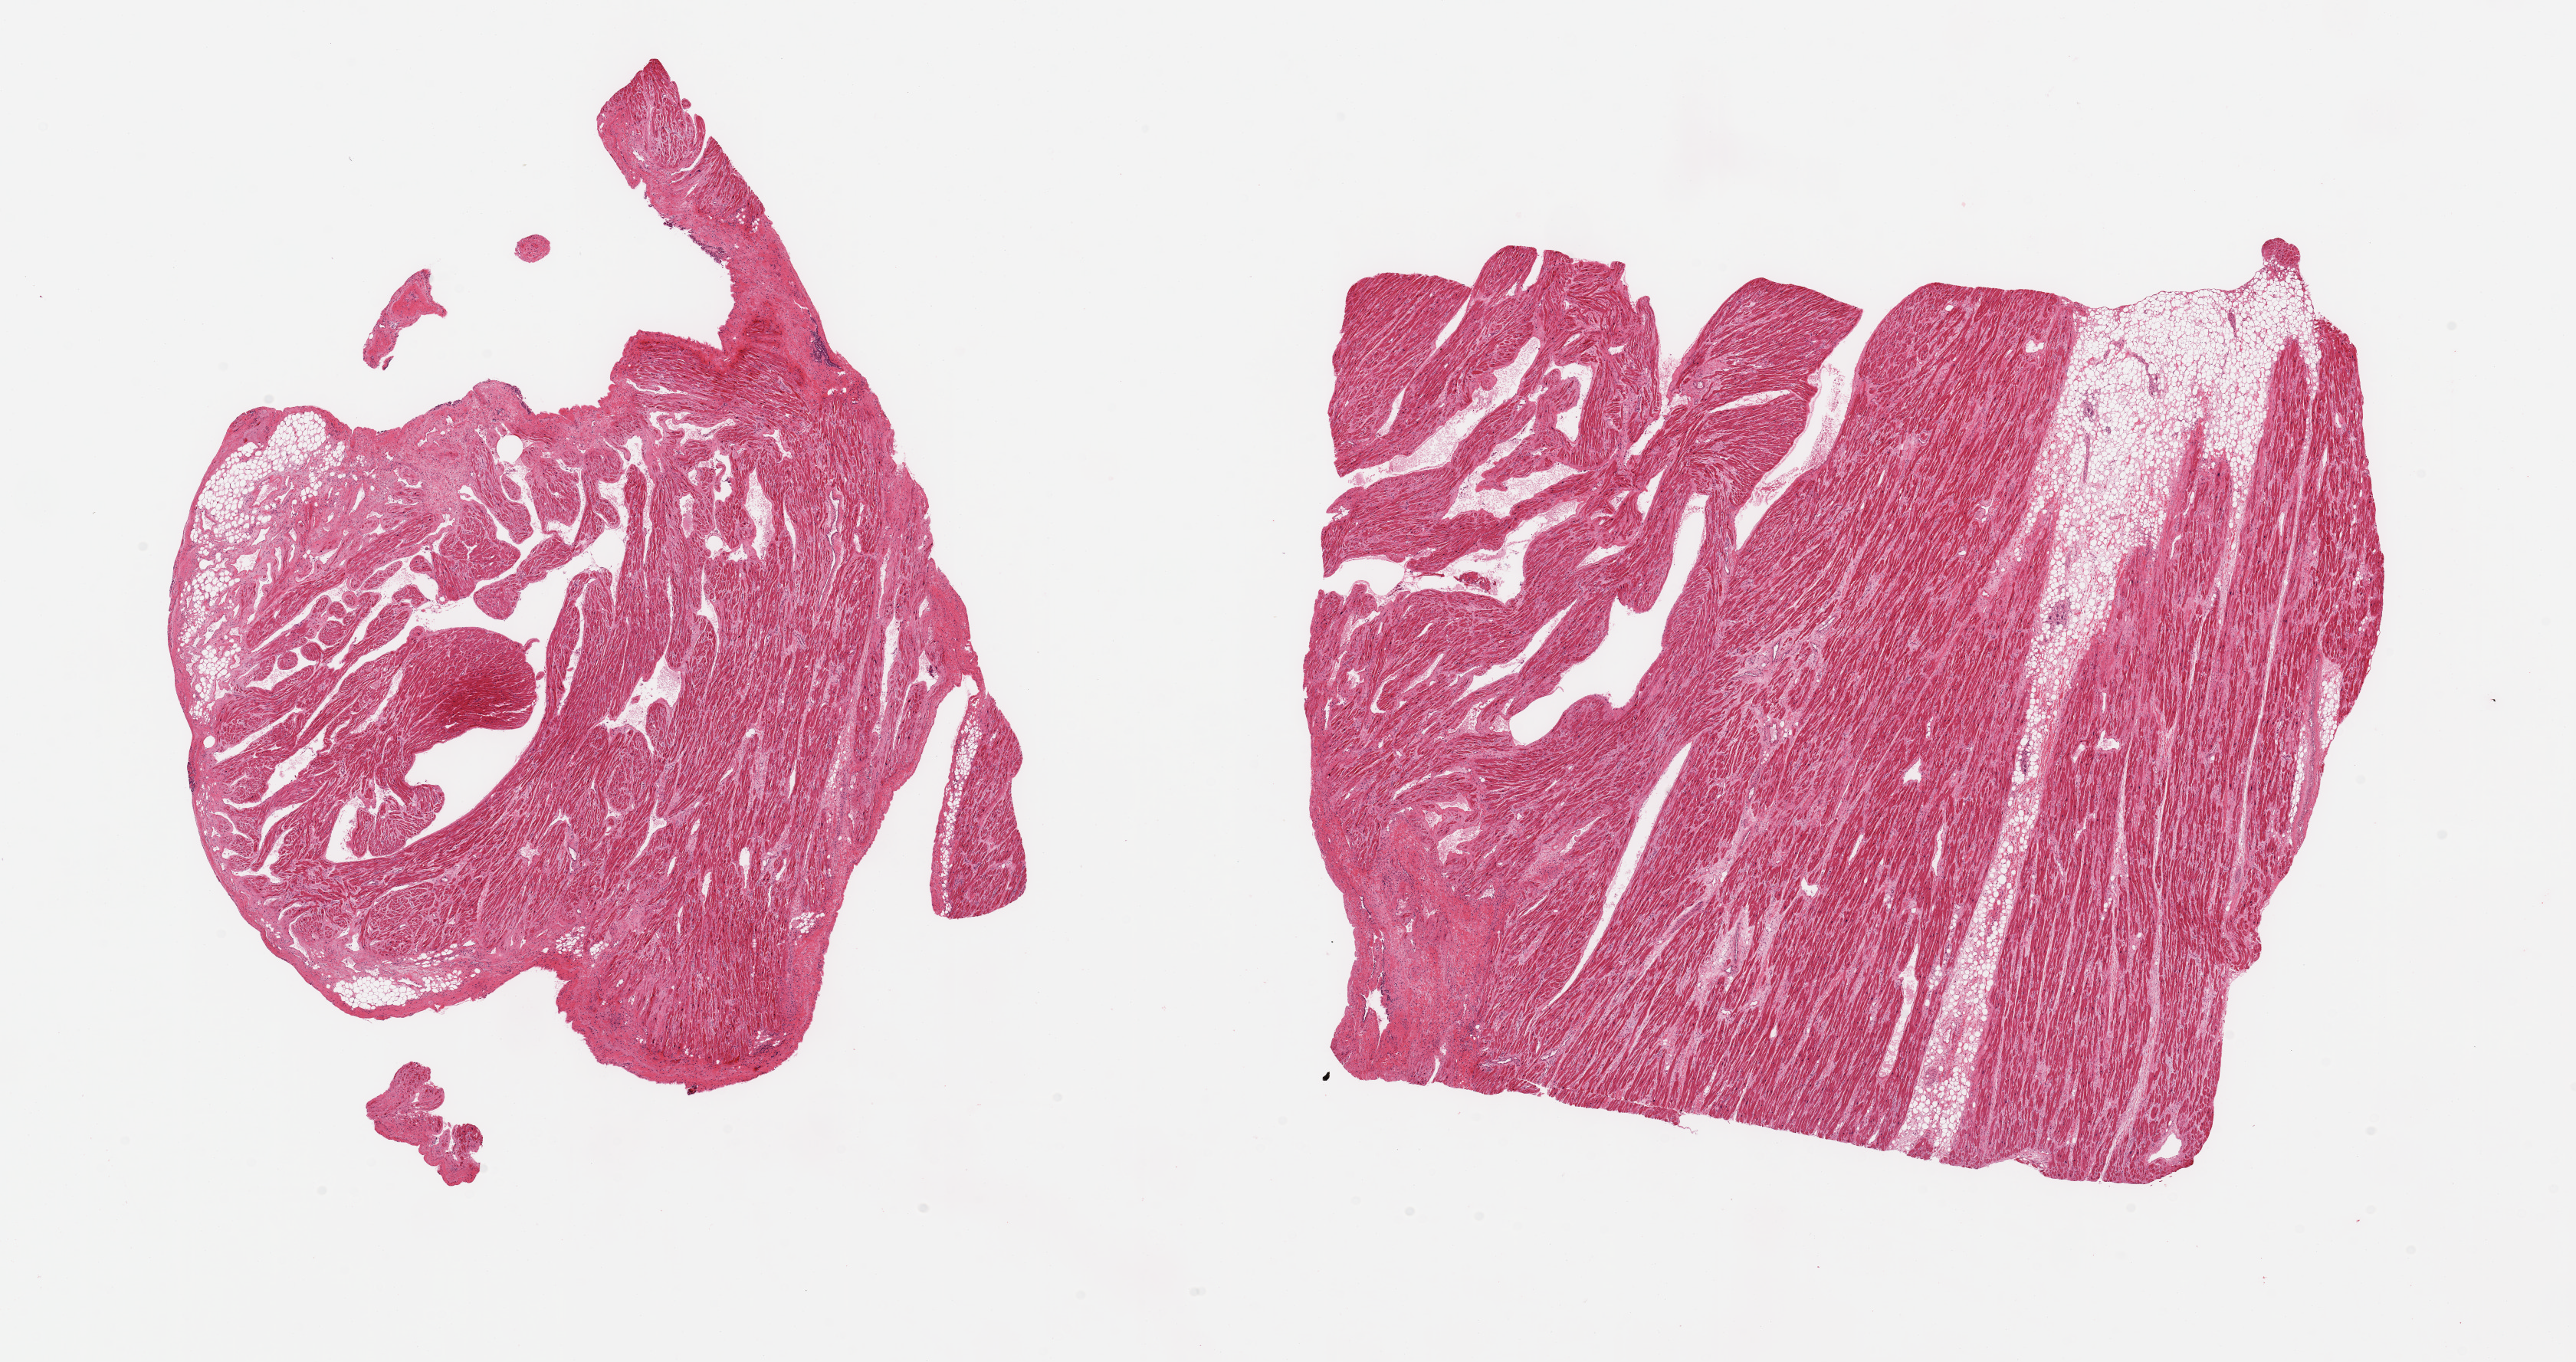
Digitized haematoxylin and eosin-stained section, brightfield, low-resolution overview of the scanned area, about 26.6 x 14.1 mm (acquisition: 20x scan). PAXgene-fixed paraffin-embedded (PFPE) section. Target tissue: auricular appendage. Donor tissue sample. Male donor.
Reviewer comment on this tissue sample: 2 pieces; 10% fat content.